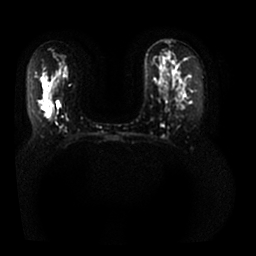
Breast MRI, one axial slice. Slice 16 of 25 in the series (ordered by position). Diffusion-weighted series; image 2 of 4 stored at this slice position (different b-values; order by instance number). 1.5 T. 4 mm slice thickness. 256 × 256 image matrix. Female patient.
Outlined on this slice (outlined manually by an expert reader):
- tumour on diffusion-weighted imaging: bounding box [x1, y1, x2, y2] px = [45, 108, 52, 118]